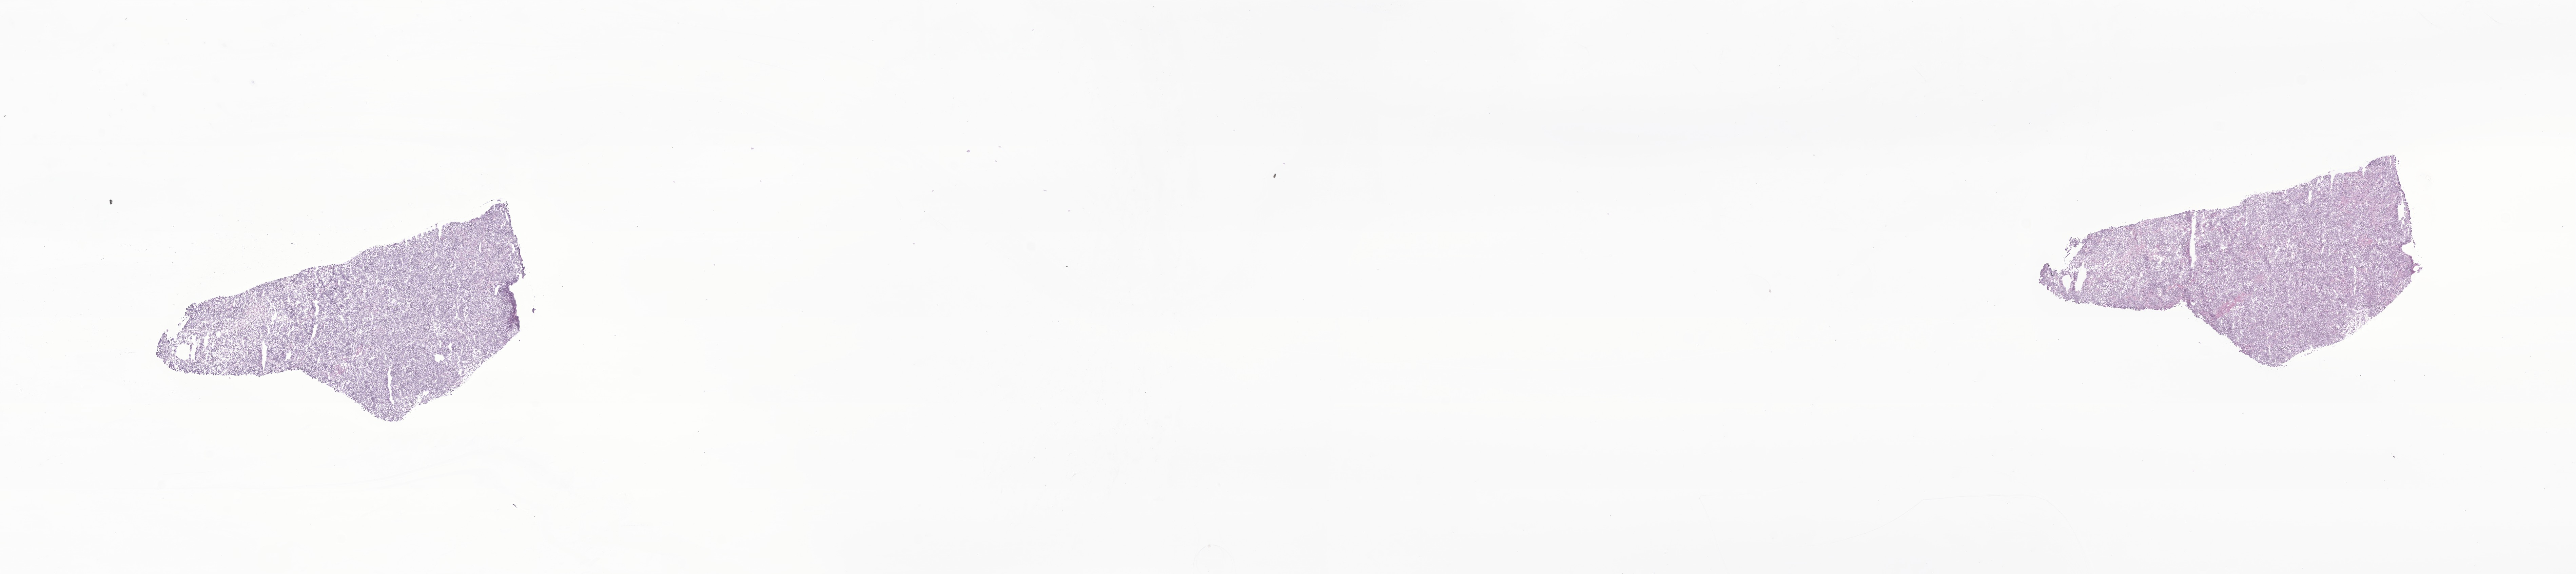
Digitized haematoxylin and eosin-stained section of tumor tissue from the cerebellum — whole scanned area (about 32.0 x 7.1 mm) shown as a low-resolution overview, frozen section (OCT-embedded). Female patient, age 140 months (11 years 8 months).
Diagnosis (ICD-O-3 morphology term): Medulloblastoma, NOS.